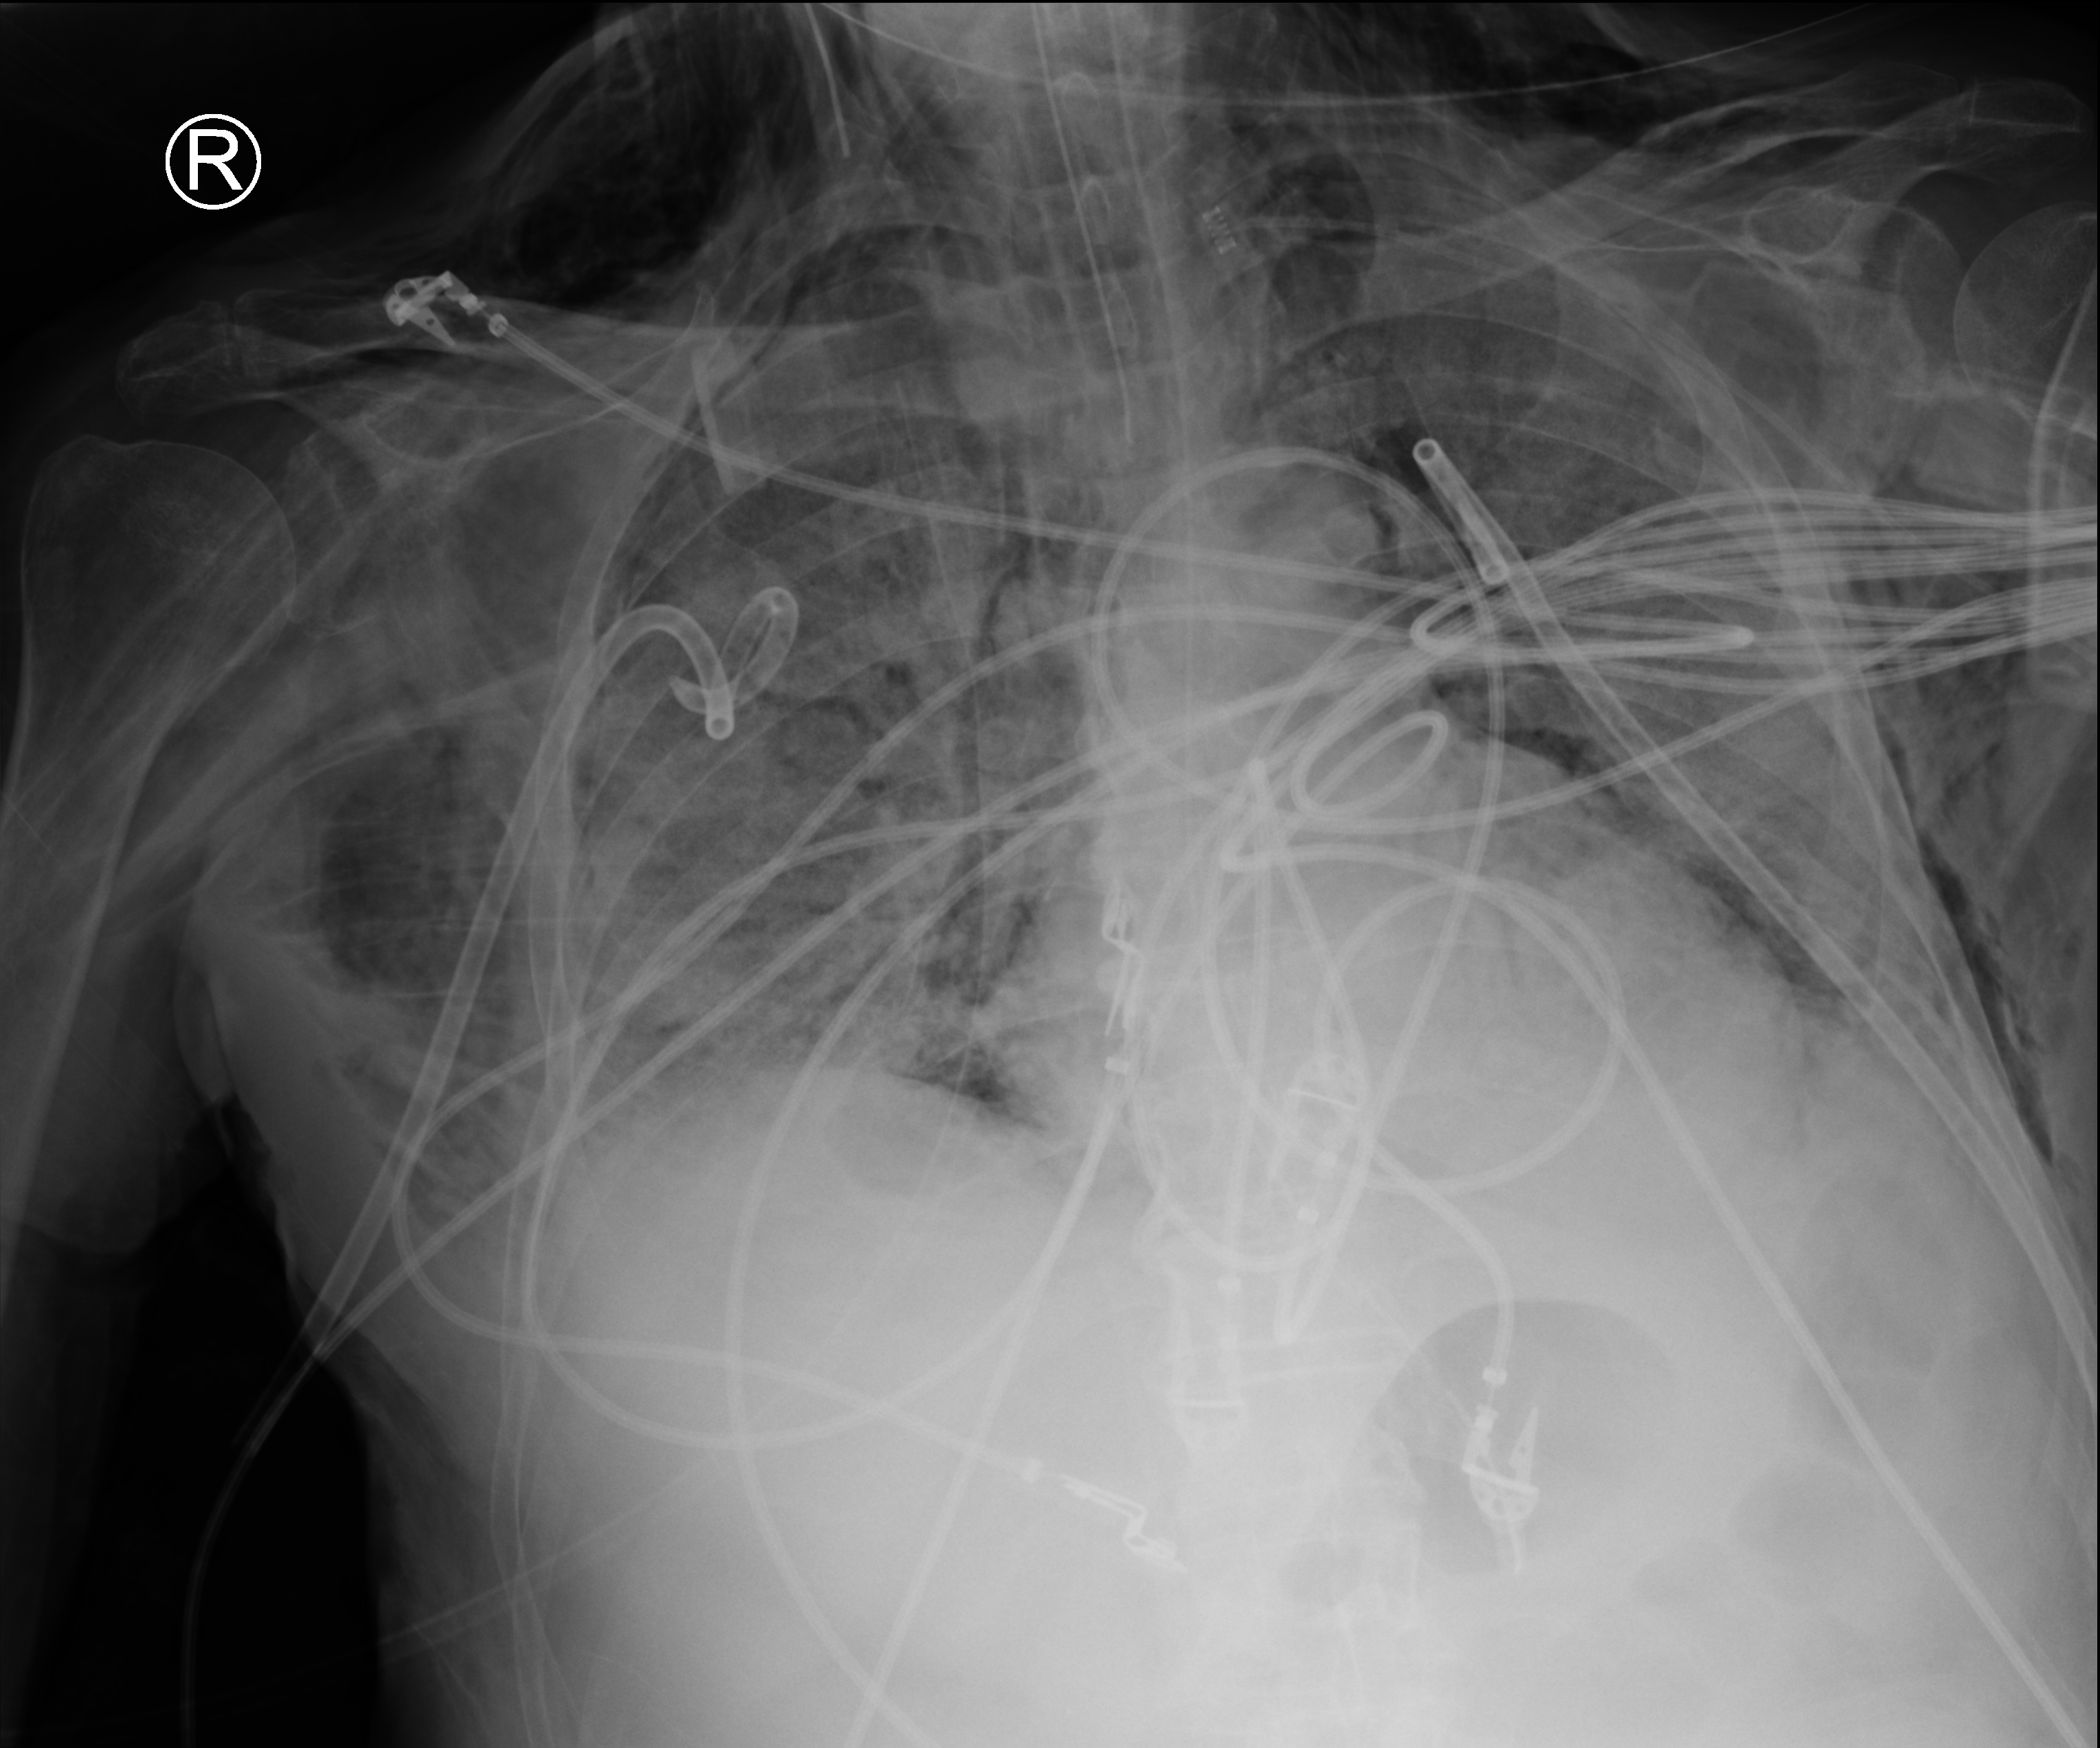
Bedside chest radiograph (computed radiography); anteroposterior (AP) projection. Patient hospitalised with COVID-19; male, aged 75–90 years.
Hospital-stay facts (about this admission, not read from this image; timing relative to this image not recorded):
- hypertension (admission record): yes
- mechanically ventilated during this hospital stay: yes
- admitted to intensive care during this hospital stay: yes